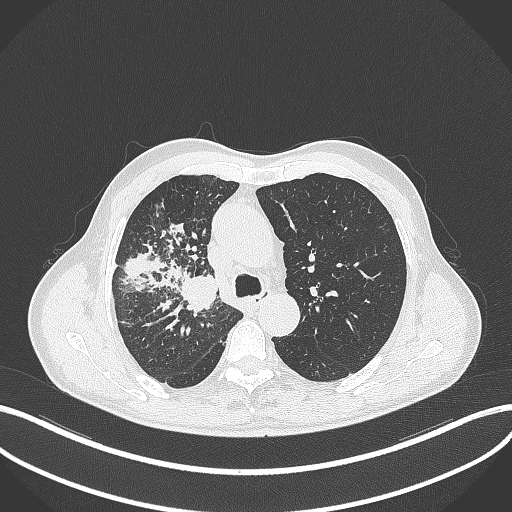
Chest CT, one axial slice. Slice 335 of 490 in the series (ordered by position). 120 kVp. Lung window (W 1500 / L -600 HU). 512 × 512 image matrix. Patient: male, 69 years. From the clinical record (not read from this slice): clinical TNM (as recorded): T2a N0 M0.
Structures marked on this image (rectangle marked by the reading radiologist):
- lung tumour (recorded histology: adenocarcinoma): bounding box <177,270,220,318> (left, top, right, bottom; pixels)